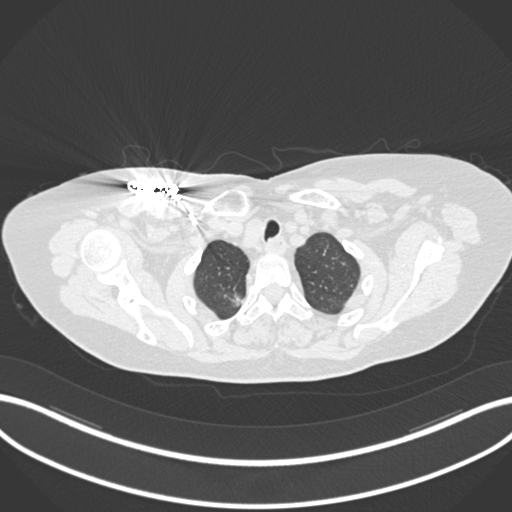
Chest CT, one axial slice. Position 162 of 176 along the scan axis. Reconstruction kernel B30f. 120 kVp. Lung window (W 1500 / L -600 HU). 1 mm slice thickness. 512 × 512 image matrix, field of view 400 × 400 mm. Female patient, age 72 years. From the clinical record (not read from this slice): clinical TNM (as recorded): T1c N0 M0.
Structures marked on this image (bounding box drawn by a radiologist):
- lung tumour (recorded histology: adenocarcinoma): bounding box [x1, y1, x2, y2] px = [223, 287, 247, 311]